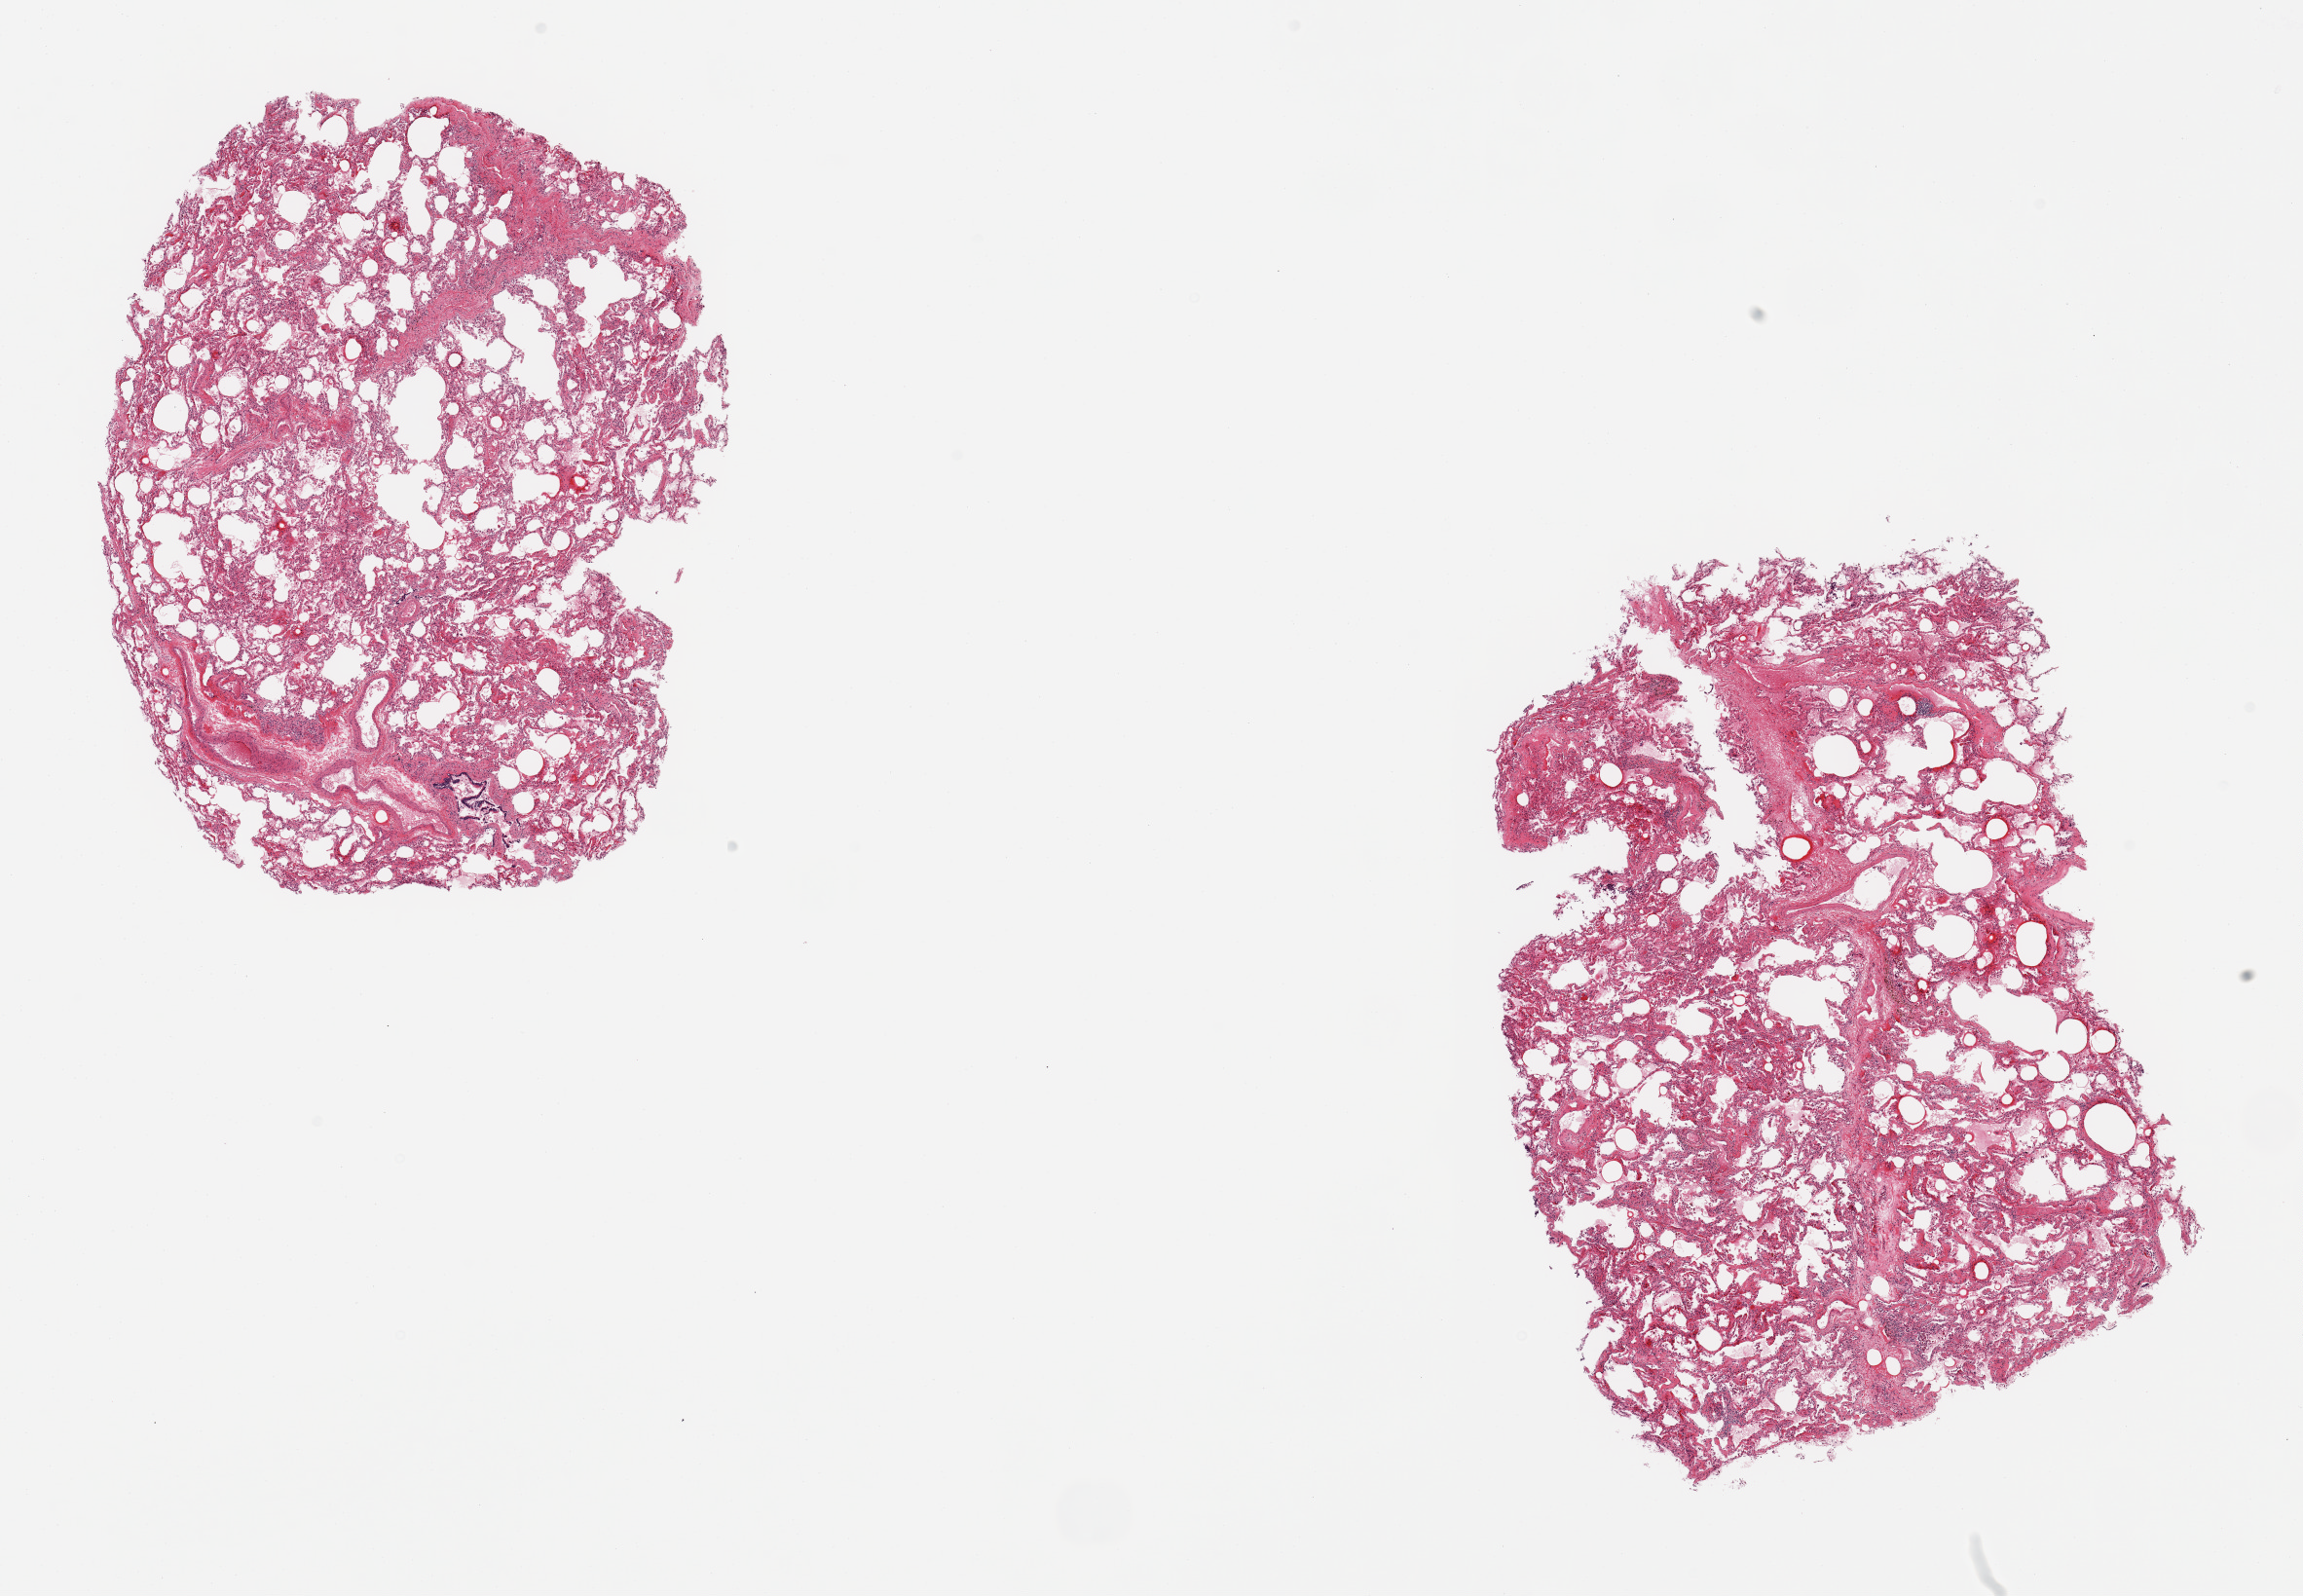
Haematoxylin and eosin whole-slide image, brightfield — whole scanned area (about 18.7 x 13.0 mm, from a 20x scan) shown as a low-resolution overview, PAXgene-fixed paraffin-embedded (PFPE) section, sampled site (target tissue): lung, donor tissue sample.
Review note (as recorded): 2 pieces, mild congestion.